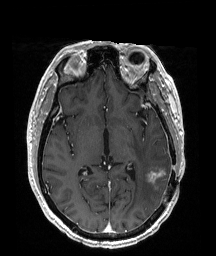
Brain MRI from a brain-tumour surgery series, one axial slice; slice 98 of 192 in the series (ordered by position); T1-weighted post-contrast; 1 mm slice thickness; 216 × 256 image matrix, field of view 211 × 250 mm. From the clinical record (not read from this slice): histopathology: Glioblastoma; WHO grade: 4; IDH mutation: no; tumour location: Left Temporoparietal.
Annotated regions visible in this slice (expert manual segmentation):
- tumour: box from (x=150, y=167) to (x=168, y=181) px